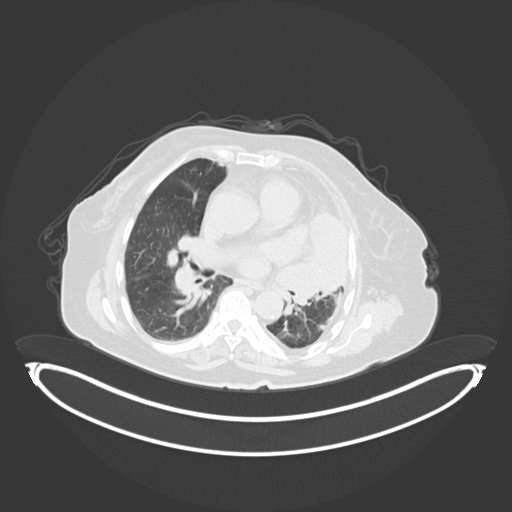
Chest CT, one axial slice; position 196 of 284 along the scan axis; lung window (W 1500 / L -600 HU); 3 mm slice thickness; 512 × 512 image matrix, field of view 500 × 500 mm. Patient: female, 75 years. Case-level facts recorded for this patient, not image findings: clinical TNM (as recorded): T3 N3 M1.
Annotated regions visible in this slice (bounding box drawn by a radiologist):
- lung tumour (recorded histology: adenocarcinoma): bounding box <276,197,354,313> (left, top, right, bottom; pixels)